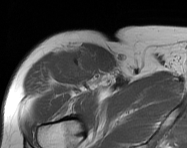
MRI of an extremity soft-tissue mass, one axial slice. Slice 110 of 114 in the series (ordered by position). MR volume resampled by the dataset authors to the PET/CT grid (not the native acquisition matrix). 3.27 mm slice thickness. 187 × 148 image matrix, field of view 183 × 145 mm. Male patient. From the clinical record (not read from this slice): histological type: pleiomorphic leiomyosarcoma; grade: intermediate; site of the primary tumour: right thigh.
Structures marked on this image (expert contour drawn on MRI and transferred to this co-registered scan by the dataset authors):
- gross tumour volume including surrounding oedema: bounding box (x1, y1, x2, y2) in pixels: (72, 52, 101, 83)